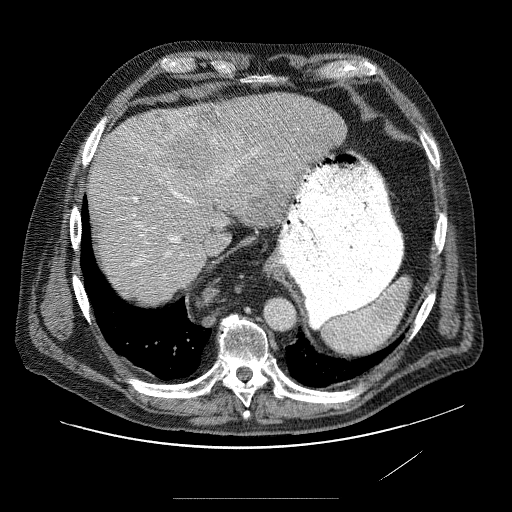
Contrast-enhanced abdominal CT (liver protocol), one axial slice; slice 64 of 89 in the series (ordered by position); soft-tissue window (W 400 / L 40 HU); 512 × 512 image matrix. From the clinical record (not read from this slice): diagnosis: hepatocellular carcinoma (patient treated with transarterial chemoembolisation; whether this scan precedes or follows treatment is not stated here); TNM stage (as recorded): Stage-IVA; Child-Pugh class: A; tumour differentiation: moderately differentiated; tumour nodularity: multinodular.
Structures marked on this image (semi-automatically segmented with operator editing):
- liver parenchyma outside the tumour (the mass and vessels are separate outlines, so this box may not span the whole liver): bounding box [x1, y1, x2, y2] px = [86, 94, 346, 284]
- mass: [149, 104, 292, 231]
- liver vessels: [132, 155, 274, 252]